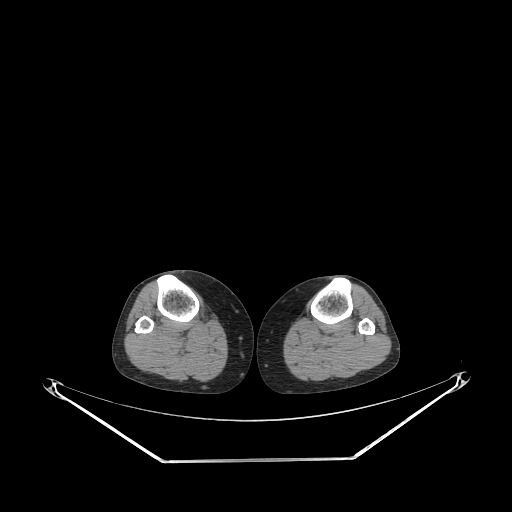
CT of an extremity soft-tissue mass (from a PET/CT study), one axial slice; slice 158 of 267 in the series (ordered by position); 140 kVp; soft-tissue window (W 400 / L 40 HU); 3.75 mm slice thickness; 512 × 512 image matrix, field of view 500 × 500 mm. Female patient. From the clinical record (not read from this slice): histological type: undifferentiated – high grade; grade: high; site of the primary tumour: right thigh.
Outlined on this slice (expert contour drawn on MRI and transferred to this co-registered scan by the dataset authors):
- gross tumour volume (mass): bounding box [x1, y1, x2, y2] px = [199, 311, 209, 323]